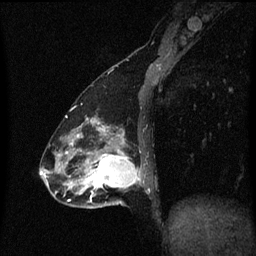
Breast MRI (dynamic contrast-enhanced), one sagittal slice; position 21 of 60 along the scan axis; dynamic contrast-enhanced series, image 2 of 3 at this slice position (ordered by acquisition); 1.5 T; TE 4.2 ms, TR 8.4 ms; 256 × 256 image matrix. Female patient, age 47 years.
Outlined on this slice (semi-automatic segmentation, software-assisted and operator-edited):
- analysis volume of interest (the breast-tissue region the enhancement analysis was run in; not a lesion): bounding box [x1, y1, x2, y2] px = [81, 138, 146, 209]
- tumour enhancement mask (voxels above the 70 % enhancement threshold inside the analysis volume of interest): [83, 140, 141, 203]